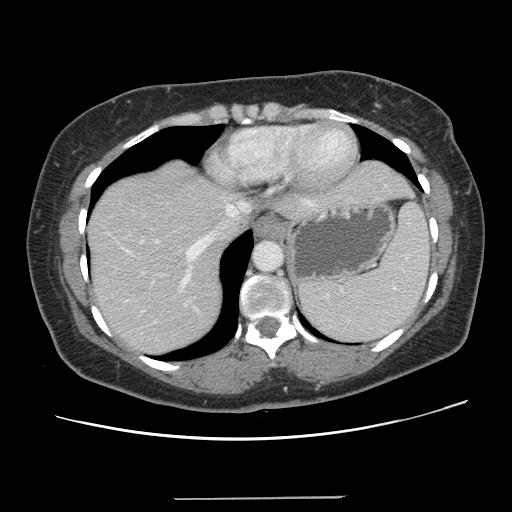
Contrast-enhanced abdominal CT, one axial slice; slice 112 of 141 in the series (ordered by position); 120 kVp; intravenous contrast given; soft-tissue window (W 400 / L 40 HU); 512 × 512 image matrix, field of view 366 × 366 mm. Female patient, age 53 years. From the clinical record (not read from this slice): diagnosis: colorectal cancer liver metastases, imaged before liver resection; multiple liver metastases: no; largest metastasis: 14.5 cm.
Annotated regions visible in this slice (outlined manually by an expert reader):
- hepatic veins: bounding box (x1, y1, x2, y2) in pixels: (113, 196, 316, 283)
- liver: (87, 160, 410, 355)
- planned liver remnant (the part of the liver to remain after resection): (87, 208, 249, 356)
- portal vein (with intrahepatic branches): (139, 239, 197, 323)